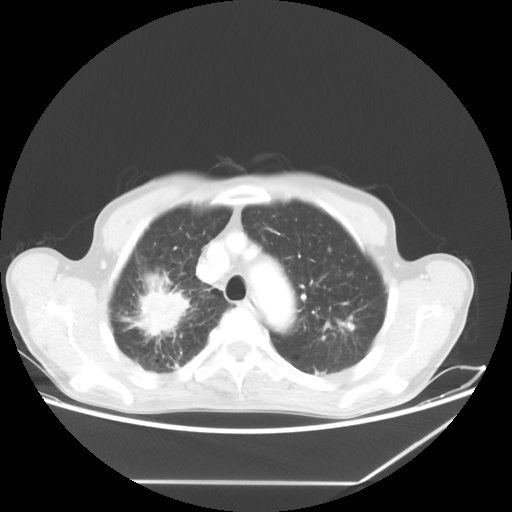
Chest CT, one axial slice; position 50 of 65 along the scan axis; reconstruction kernel STANDARD; lung window (W 1500 / L -600 HU); 5 mm slice thickness; 512 × 512 image matrix. Male patient, age 68 years. From the clinical record (not read from this slice): clinical TNM (as recorded): T3 N3 M0.
Outlined on this slice (bounding box drawn by a radiologist):
- lung tumour (recorded histology: adenocarcinoma): bounding box <128,269,188,348> (left, top, right, bottom; pixels)